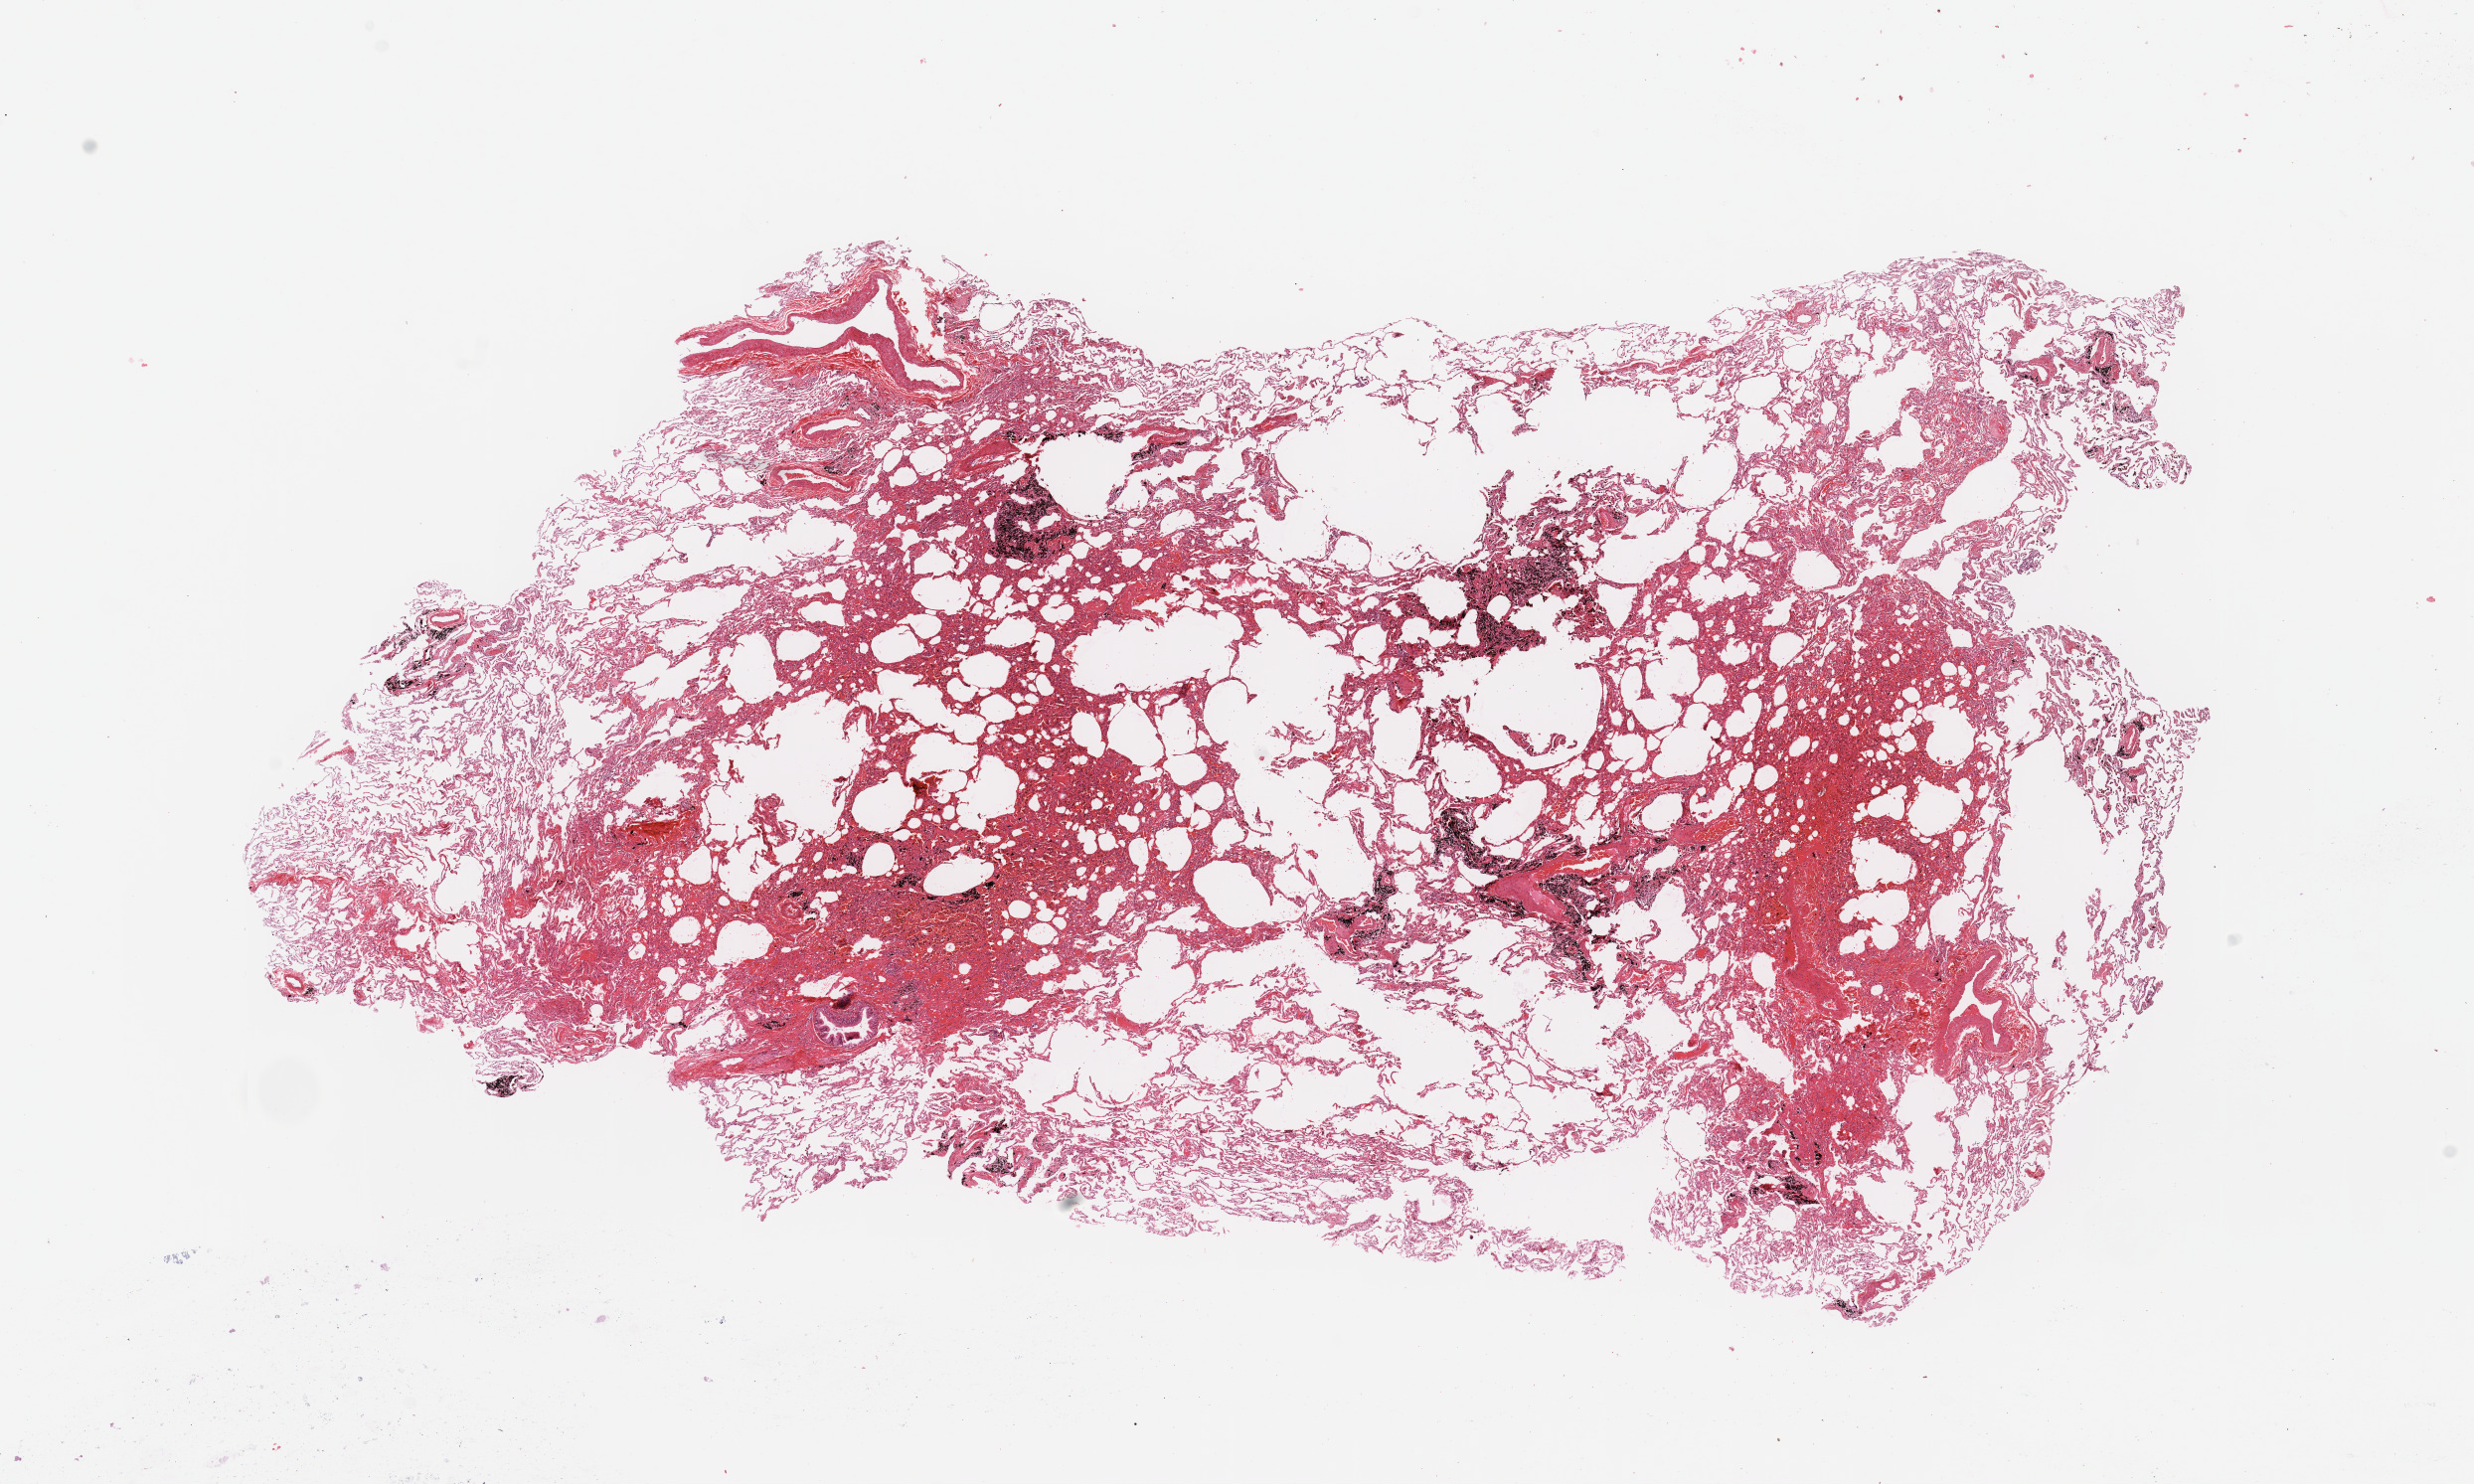
Digitized Hematoxylin and eosin (H&E) stained tissue section (whole slide), shown as a low-resolution overview of the whole scanned area (about 19.7 x 11.8 mm, slide scanned at 20x); normal (non-tumour) tissue sample, sampled site: lung. 62-year-old male patient.
• this section: normal (non-tumour) tissue from the same patient
• patient diagnosis: Squamous cell carcinoma, NOS